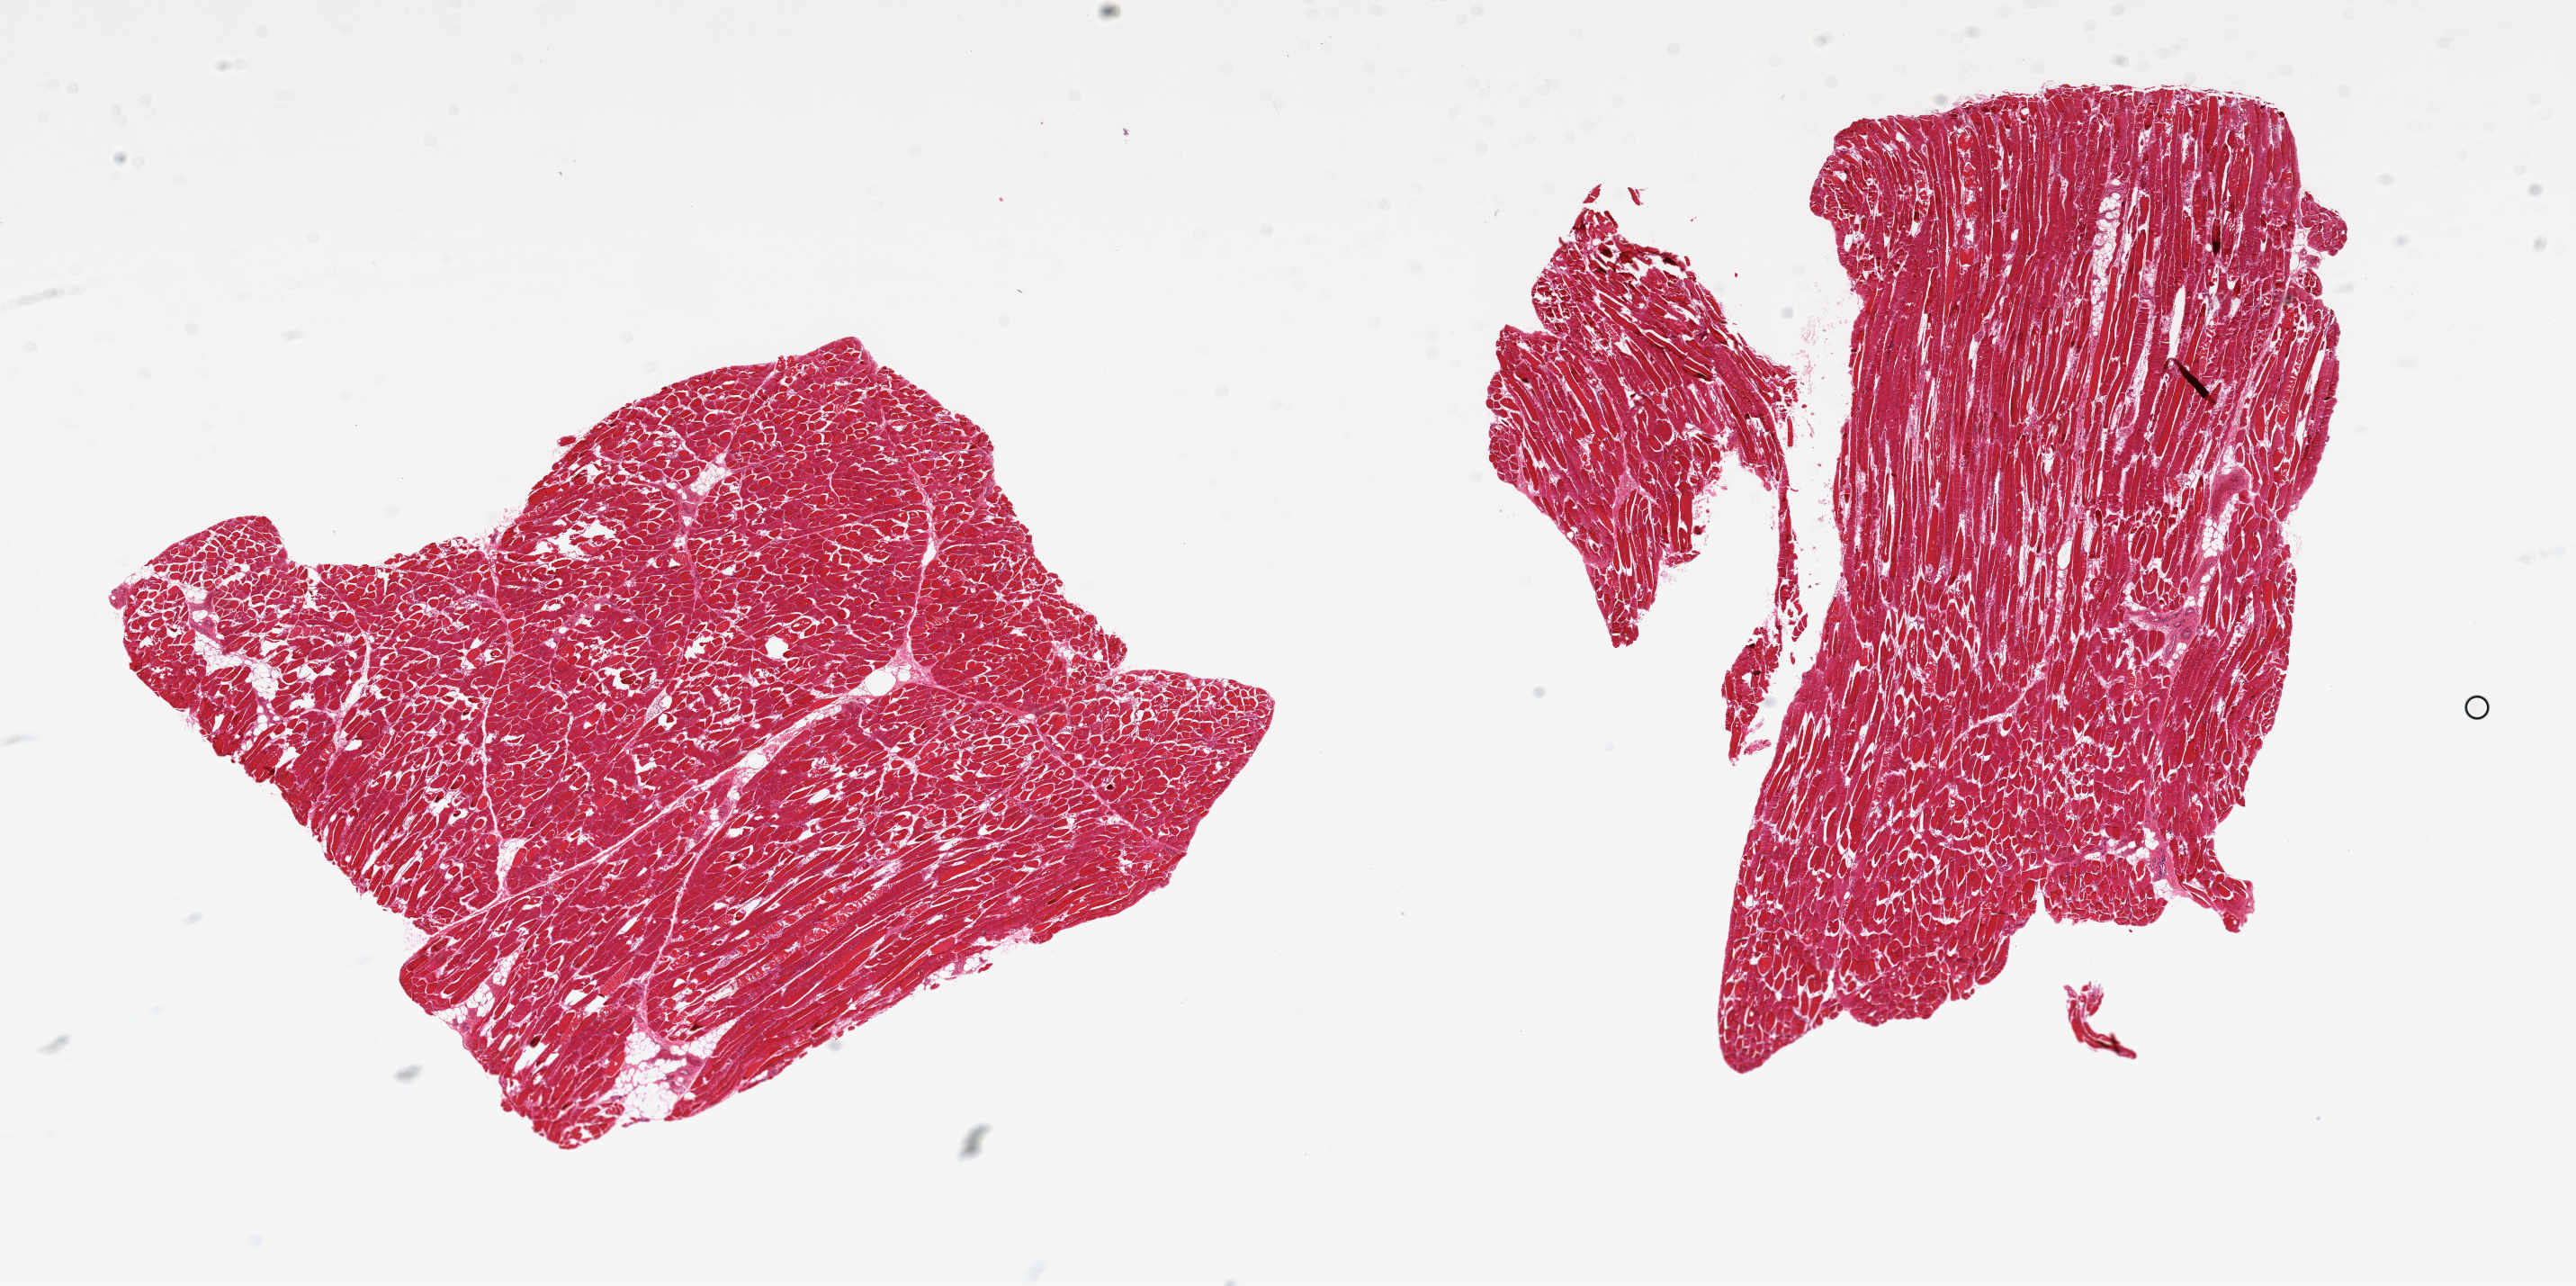
Digitized H&E-stained section, brightfield — whole scanned area (about 22.6 x 11.3 mm) shown as a low-resolution overview; PAXgene-fixed, paraffin-embedded tissue; section of skeletal muscle (target tissue); donor tissue sample. Donor sex: male.
Review note (as recorded): 2 pieces, 8x6mm unusually badly autolyzed.